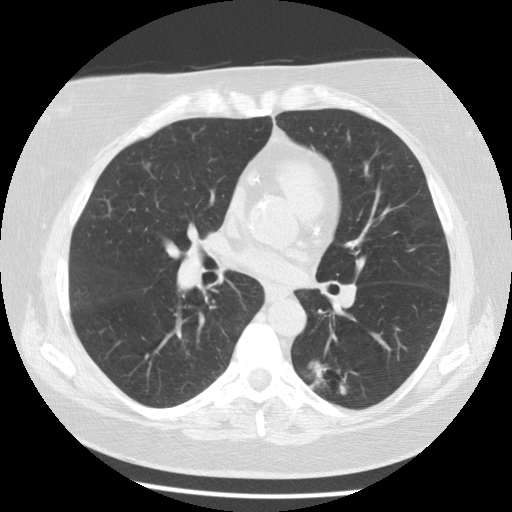
Axial slice from a low-dose chest CT screening exam. Third annual screen. Lung window (W 1500 / L -600 HU). 2.5 mm slice thickness. Standard (soft-tissue) reconstruction kernel (STANDARD). Slice 57 of 116 in the series. Female participant, aged 59 years at enrolment. Current smoker at enrolment.
Expert-annotated lung lesion, bounding box (x1, y1, x2, y2) in pixels: (297, 348, 359, 406). The screening reader recorded 6 non-calcified nodules or masses ≥4 mm on this exam; which of them this box marks is not recorded. Official screen result: positive, other. Participant outcome: lung cancer diagnosed 56 days after this screen — adenocarcinoma, NOS, left lower lobe, poorly differentiated (G3), stage IA (AJCC 6th edition), 15 mm at pathology.